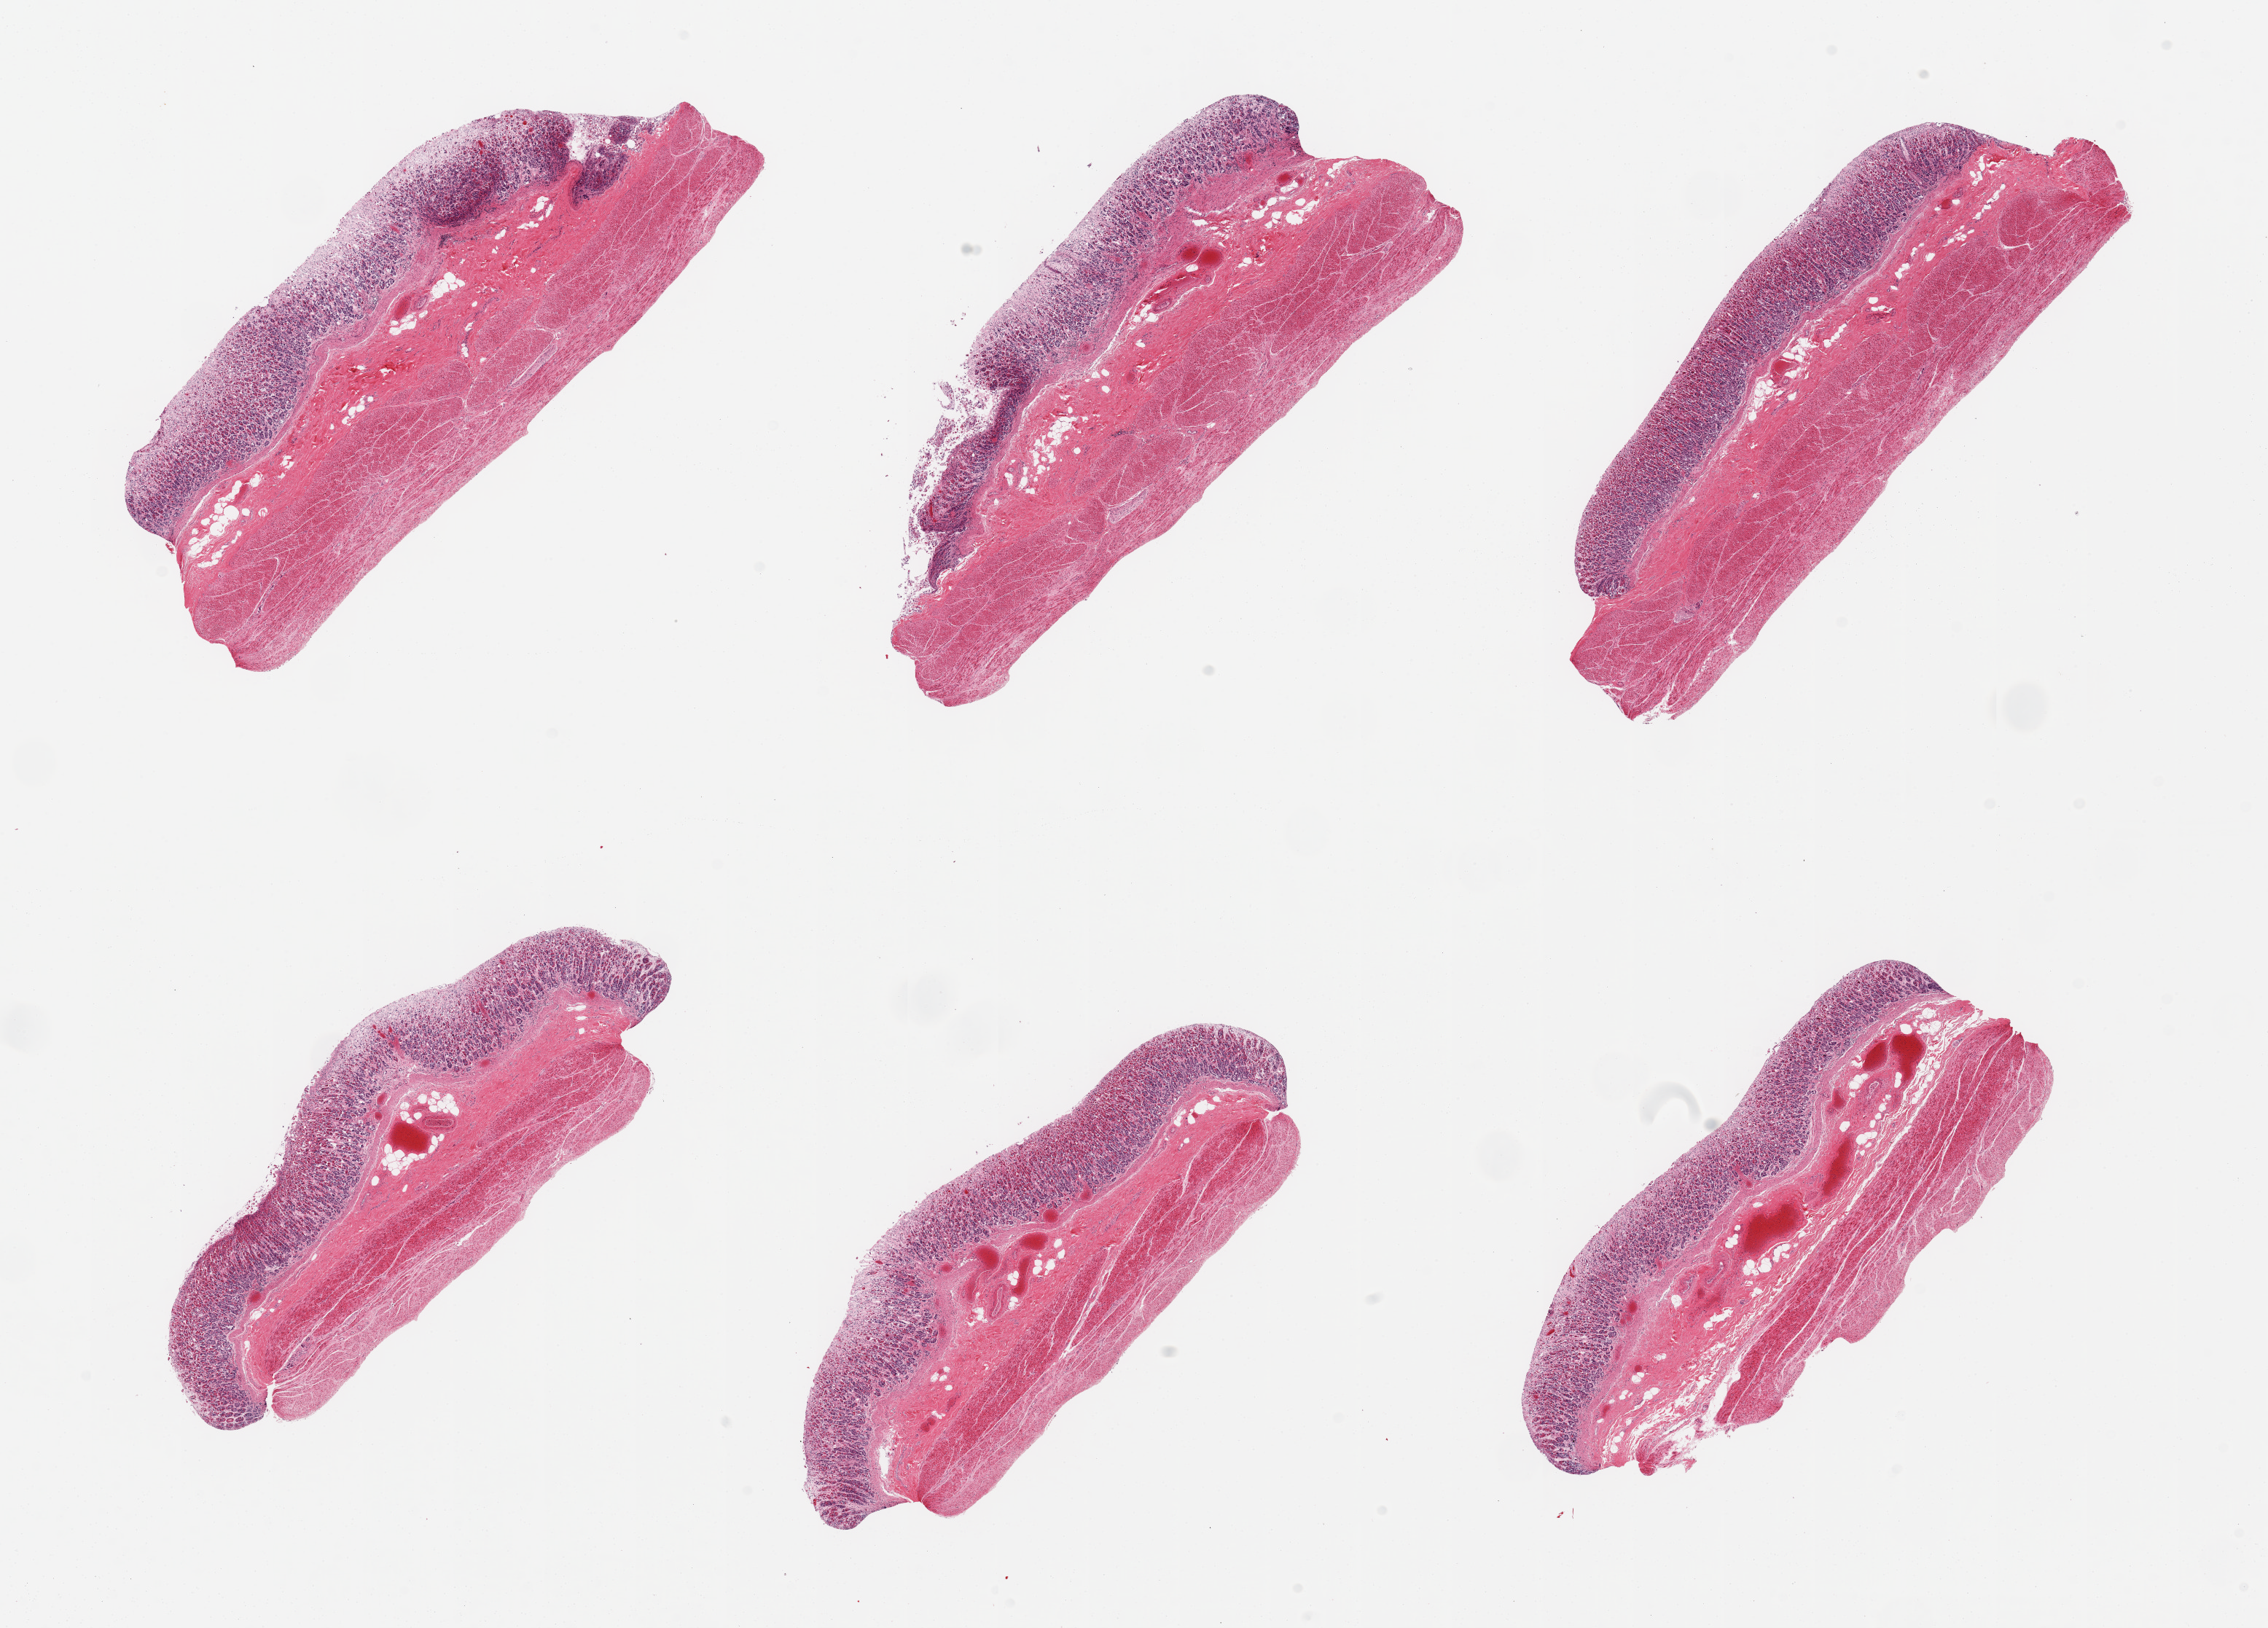
Haematoxylin and eosin whole-slide image — whole scanned area (about 24.6 x 17.7 mm, from a 20x scan) shown as a low-resolution overview, PAXgene-fixed paraffin-embedded (PFPE) section, target tissue: stomach, donor tissue sample. Donor: female.
Reviewer comment on this tissue sample: 6 pieces, moderately autolyzed mucosa and muscularis.